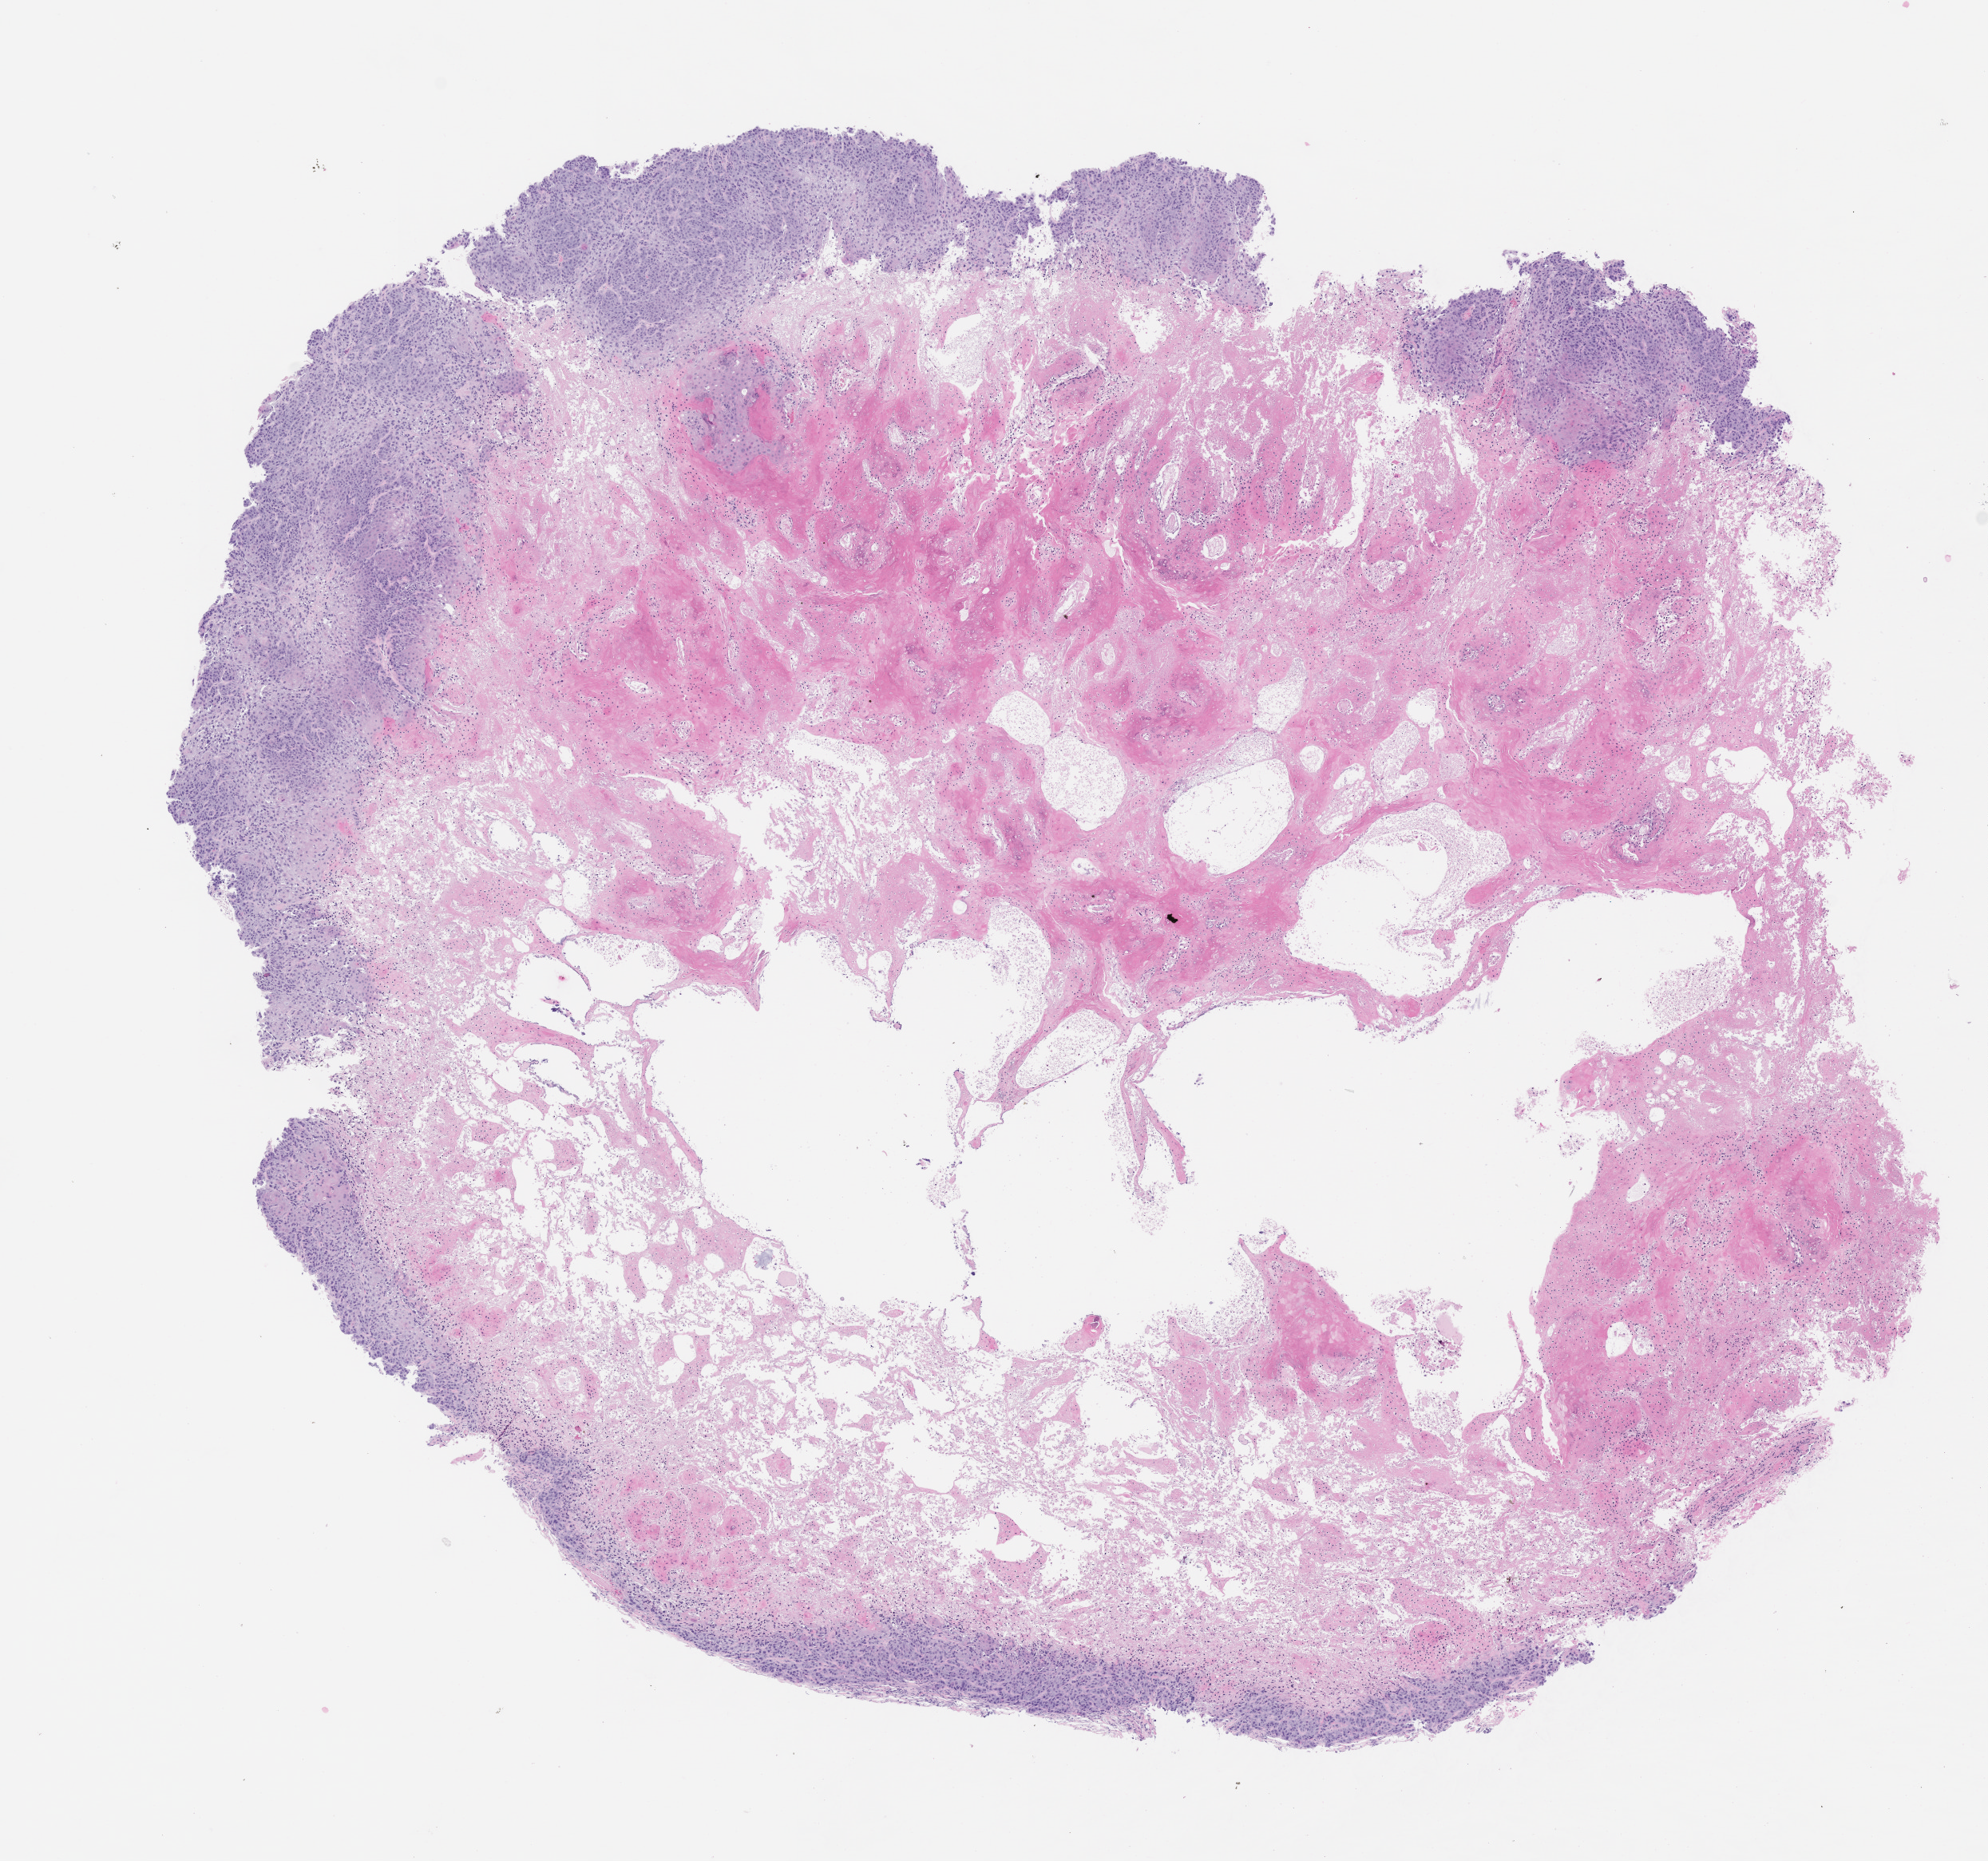
Whole-slide image, haematoxylin and eosin: patient-derived xenograft (human tumor grown in a mouse), passage 3 — shown as a low-resolution overview of the whole scanned area (about 10.0 x 9.4 mm), formalin-fixed paraffin-embedded section, tumor site category: oral soft tissue.
Originating patient diagnosis: Head and Neck Squamous Cell Carcinoma.